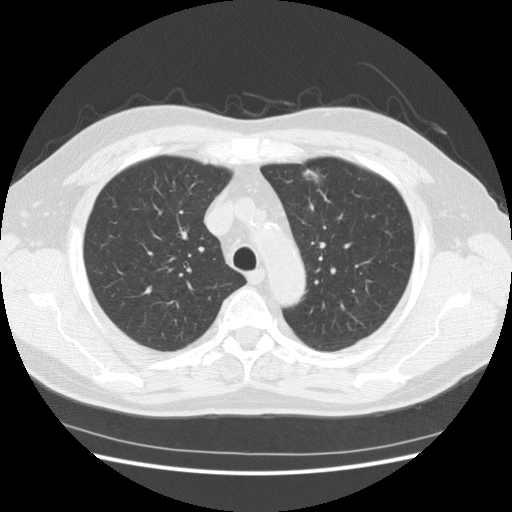
Low-dose screening chest CT, axial slice; baseline annual screen; lung window (W 1500 / L -600 HU); 2.5 mm slice thickness. Male participant, aged 63 years at enrolment. Former smoker at enrolment.
Lesion marked by an expert reader, bounding box <281,155,338,205> (left, top, right, bottom; pixels). Reader record for this screening exam (exam-level; its link to the box is not recorded): non-calcified nodule or mass ≥4 mm, lingula, 18 × 9 mm, poorly defined margins, soft tissue attenuation. Lung cancer was diagnosed 475 days after this screen: adenocarcinoma, NOS, left upper lobe, moderately differentiated (G2), stage IA (AJCC 6th edition), 14 mm at pathology.